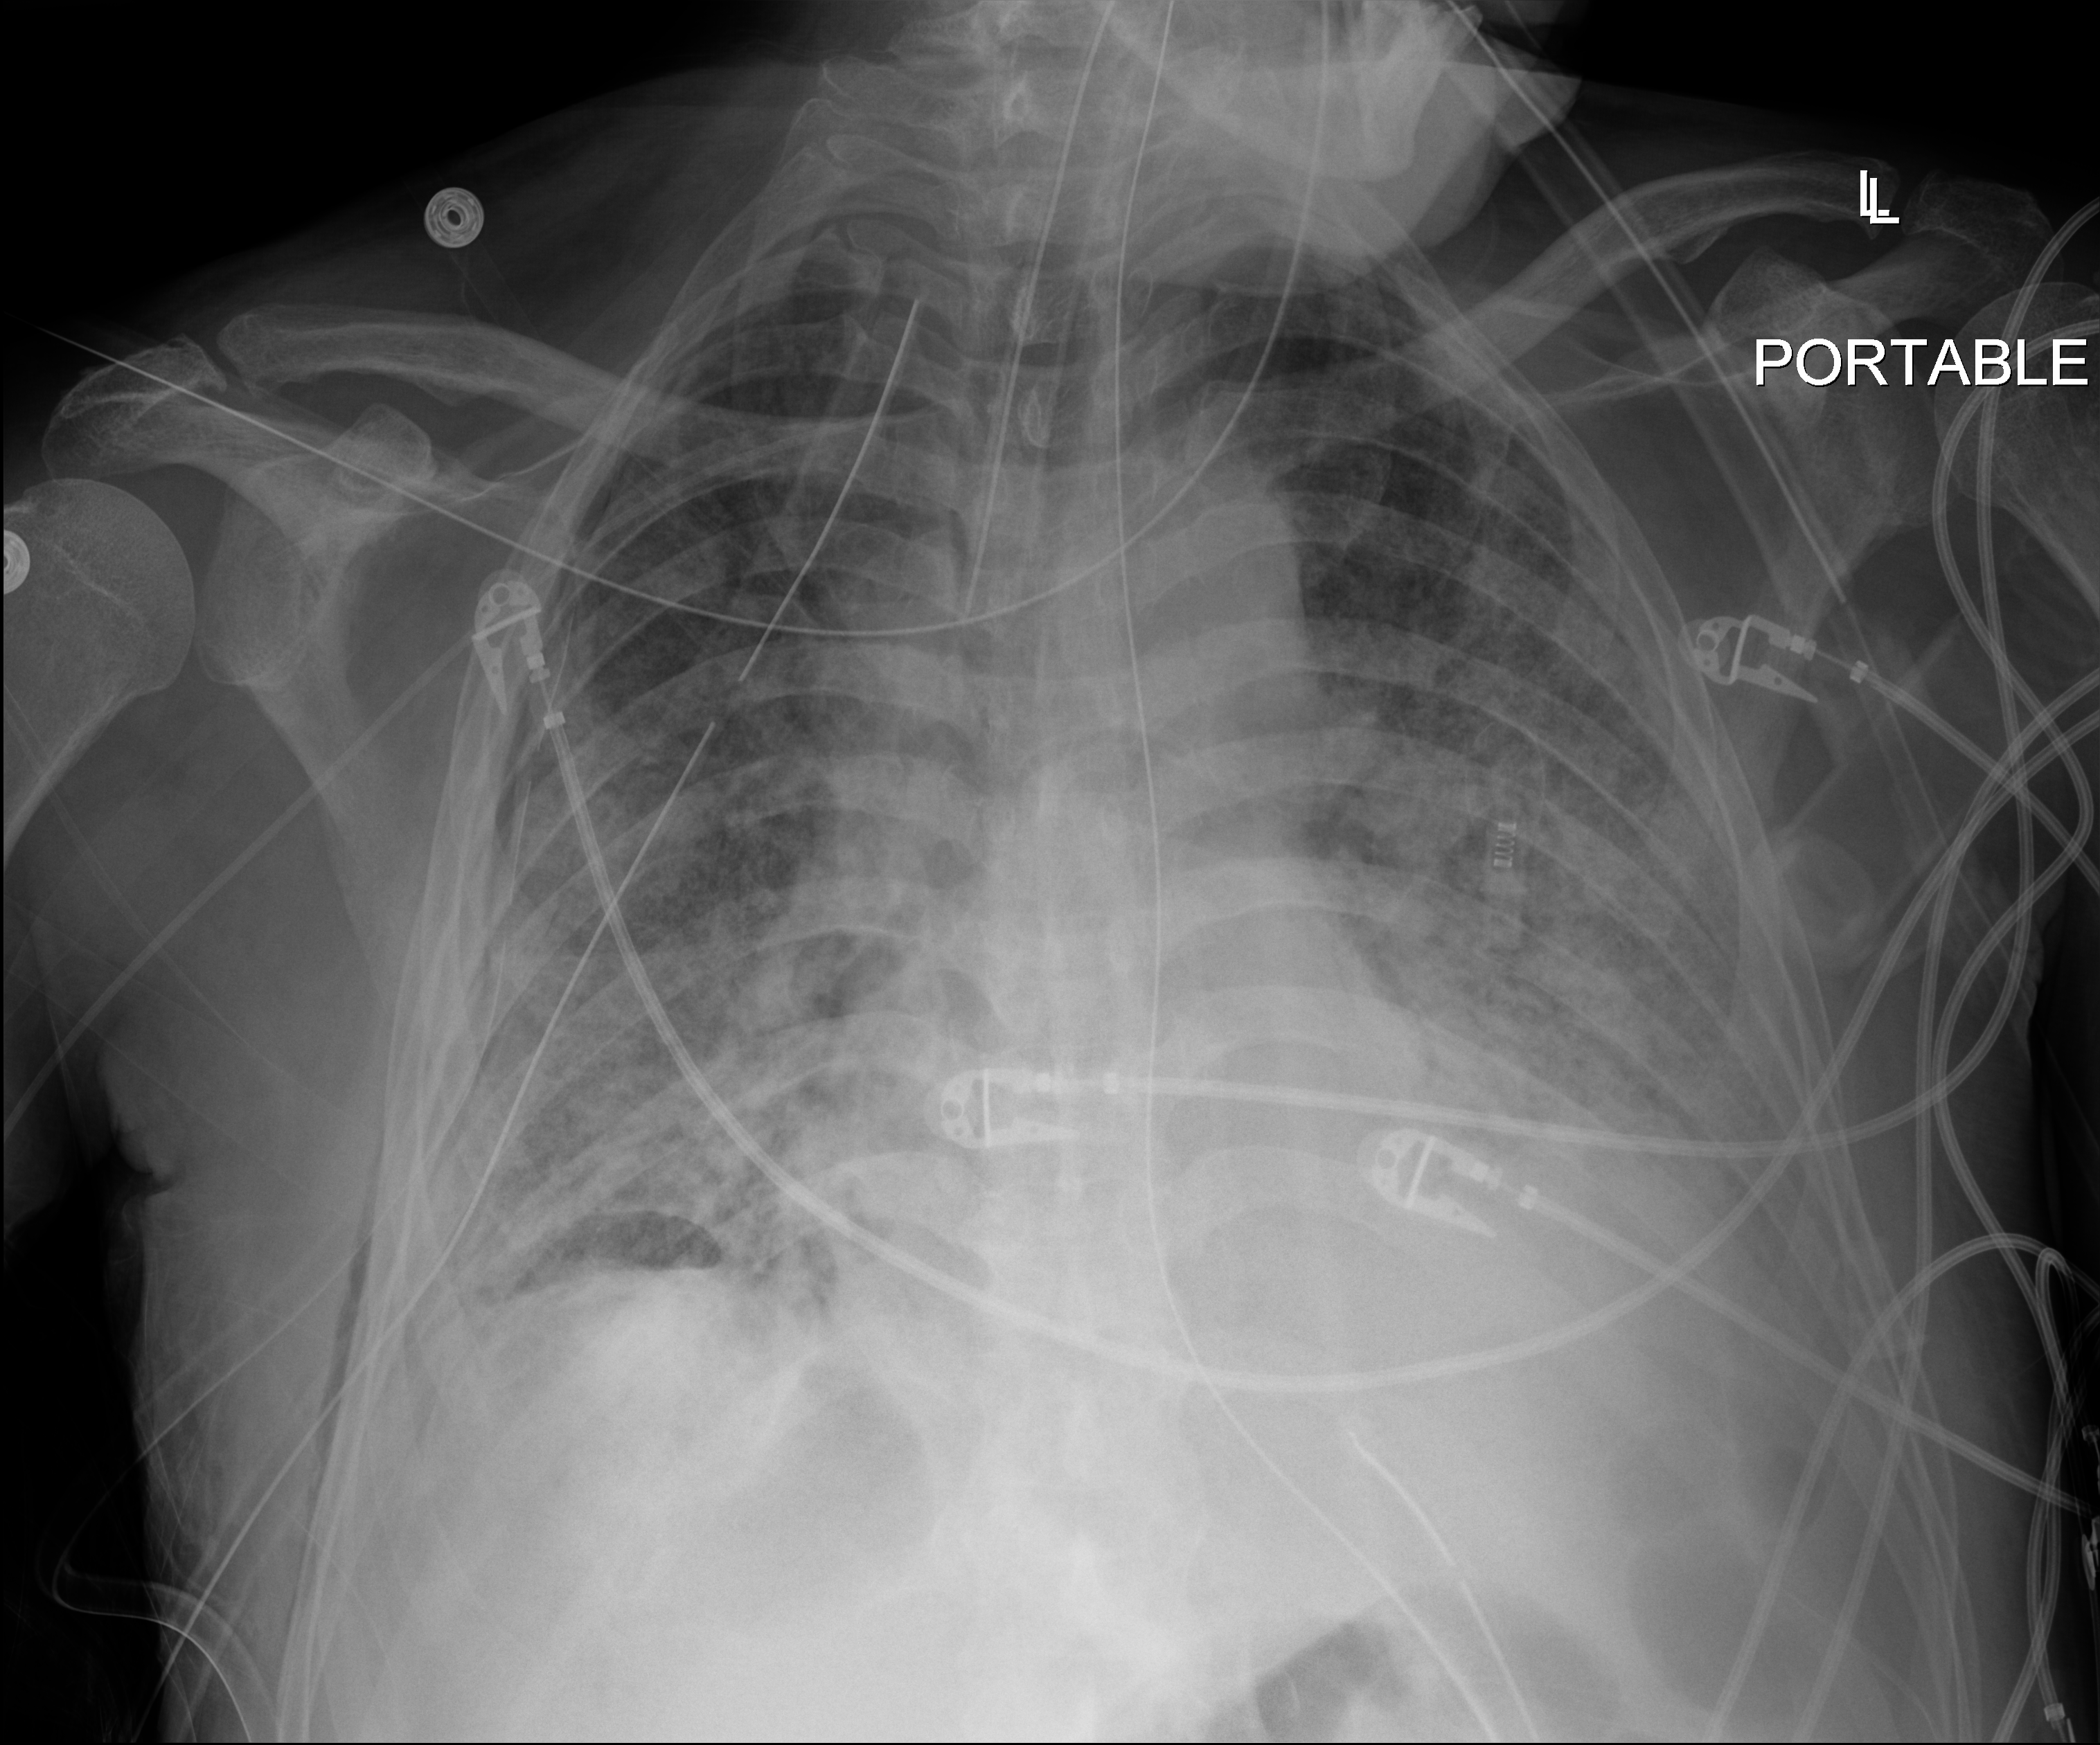
Chest X-ray; anteroposterior (AP) projection. Male patient hospitalised with COVID-19, age 60–74 years.
Hospital-stay facts (about this admission, not read from this image; timing relative to this image not recorded): mechanically ventilated during this hospital stay: yes; length of hospital stay: 37 days; admitted to intensive care during this hospital stay: yes.